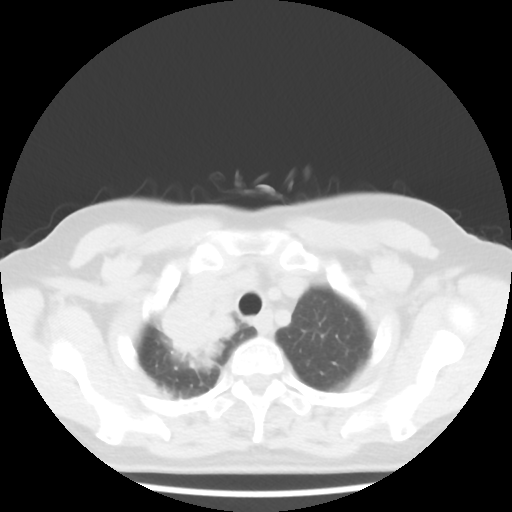
Chest CT, one axial slice; slice 37 of 43 in the series (ordered by position); 100 kVp; lung window (W 1500 / L -600 HU); 5 mm slice thickness; 512 × 512 image matrix, field of view 316 × 316 mm. Female patient, age 62 years. Case-level facts recorded for this patient, not image findings: clinical TNM (as recorded): T3 N0 M0; histopathological grade: G3.
Structures marked on this image (rectangle marked by the reading radiologist):
- lung tumour (recorded histology: small cell carcinoma): bounding box [x1, y1, x2, y2] px = [143, 262, 246, 371]